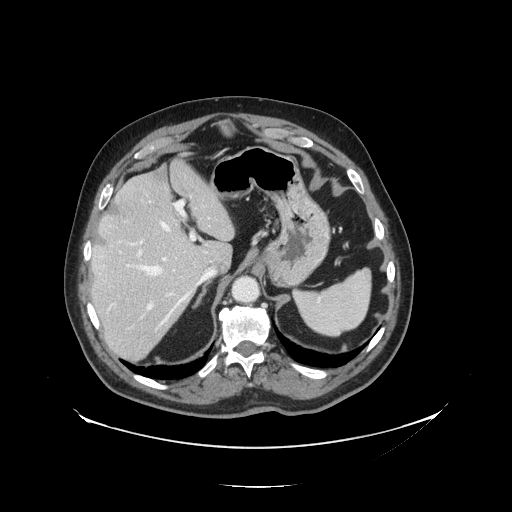
Contrast-enhanced abdominal CT, one axial slice; position 98 of 138 along the scan axis; reconstruction kernel STANDARD; intravenous contrast given; soft-tissue window (W 400 / L 40 HU); 2.5 mm slice thickness; 512 × 512 image matrix, field of view 497 × 497 mm. Male patient, age 77 years. Case-level facts recorded for this patient, not image findings: diagnosis: colorectal cancer liver metastases, imaged before liver resection; multiple liver metastases: no; largest metastasis: 1.5 cm; disease in both lobes: no.
Structures marked on this image (manually delineated by an expert):
- hepatic veins: bounding box [x1, y1, x2, y2] px = [136, 221, 210, 324]
- liver: [91, 163, 234, 361]
- planned liver remnant (the part of the liver to remain after resection): [92, 162, 234, 288]
- portal vein (with intrahepatic branches): [130, 201, 210, 311]